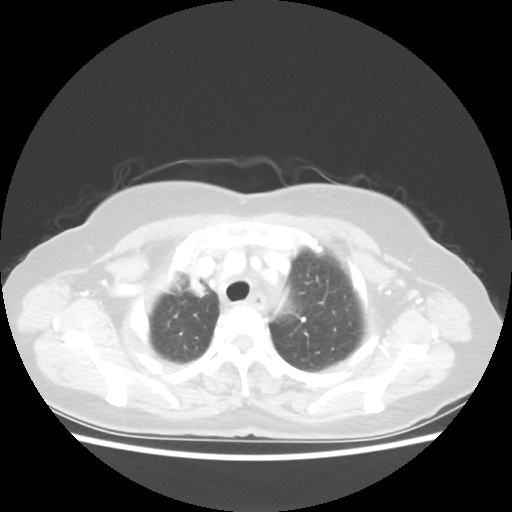
Chest CT, one axial slice; position 44 of 55 along the scan axis; reconstruction kernel STANDARD; lung window (W 1500 / L -600 HU); 512 × 512 image matrix, field of view 337 × 337 mm. Female patient, age 62 years. From the clinical record (not read from this slice): clinical TNM (as recorded): T4 N3 M0.
Annotated regions visible in this slice (rectangle marked by the reading radiologist):
- lung tumour (recorded histology: squamous cell carcinoma): bounding box [x1, y1, x2, y2] px = [149, 251, 218, 309]